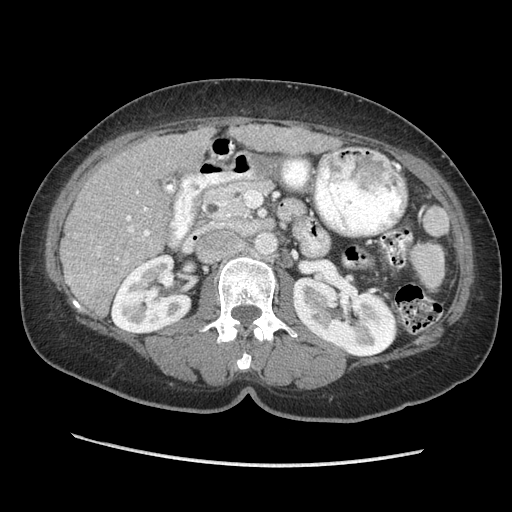
Contrast-enhanced abdominal CT (liver protocol), one axial slice; slice 114 of 170 in the series (ordered by position); 140 kVp; soft-tissue window (W 400 / L 40 HU); 512 × 512 image matrix. Case-level facts recorded for this patient, not image findings: diagnosis: hepatocellular carcinoma (patient treated with transarterial chemoembolisation; whether this scan precedes or follows treatment is not stated here); TNM stage (as recorded): Stage-II; Child-Pugh class: A; tumour nodularity: multinodular; tumour size: 4 cm.
Outlined on this slice (semi-automatic segmentation, software-assisted and operator-edited):
- liver parenchyma outside the tumour (the mass and vessels are separate outlines, so this box may not span the whole liver): bounding box (x1, y1, x2, y2) in pixels: (60, 124, 340, 316)
- liver vessels: (94, 185, 172, 272)